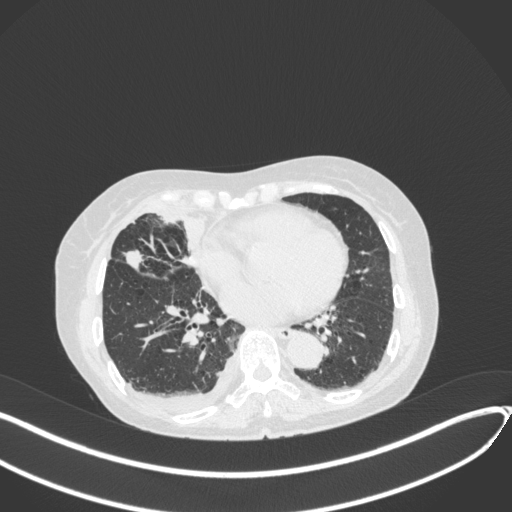
Chest CT, one axial slice. Slice 159 of 418 in the series (ordered by position). Reconstruction kernel B31f. Lung window (W 1500 / L -600 HU). 1 mm slice thickness. 512 × 512 image matrix. Female patient, age 75 years. Case-level facts recorded for this patient, not image findings: clinical TNM (as recorded): T2a N3 M0.
Annotated regions visible in this slice (rectangle marked by the reading radiologist):
- lung tumour (recorded histology: adenocarcinoma): box from (x=125, y=245) to (x=148, y=274) px